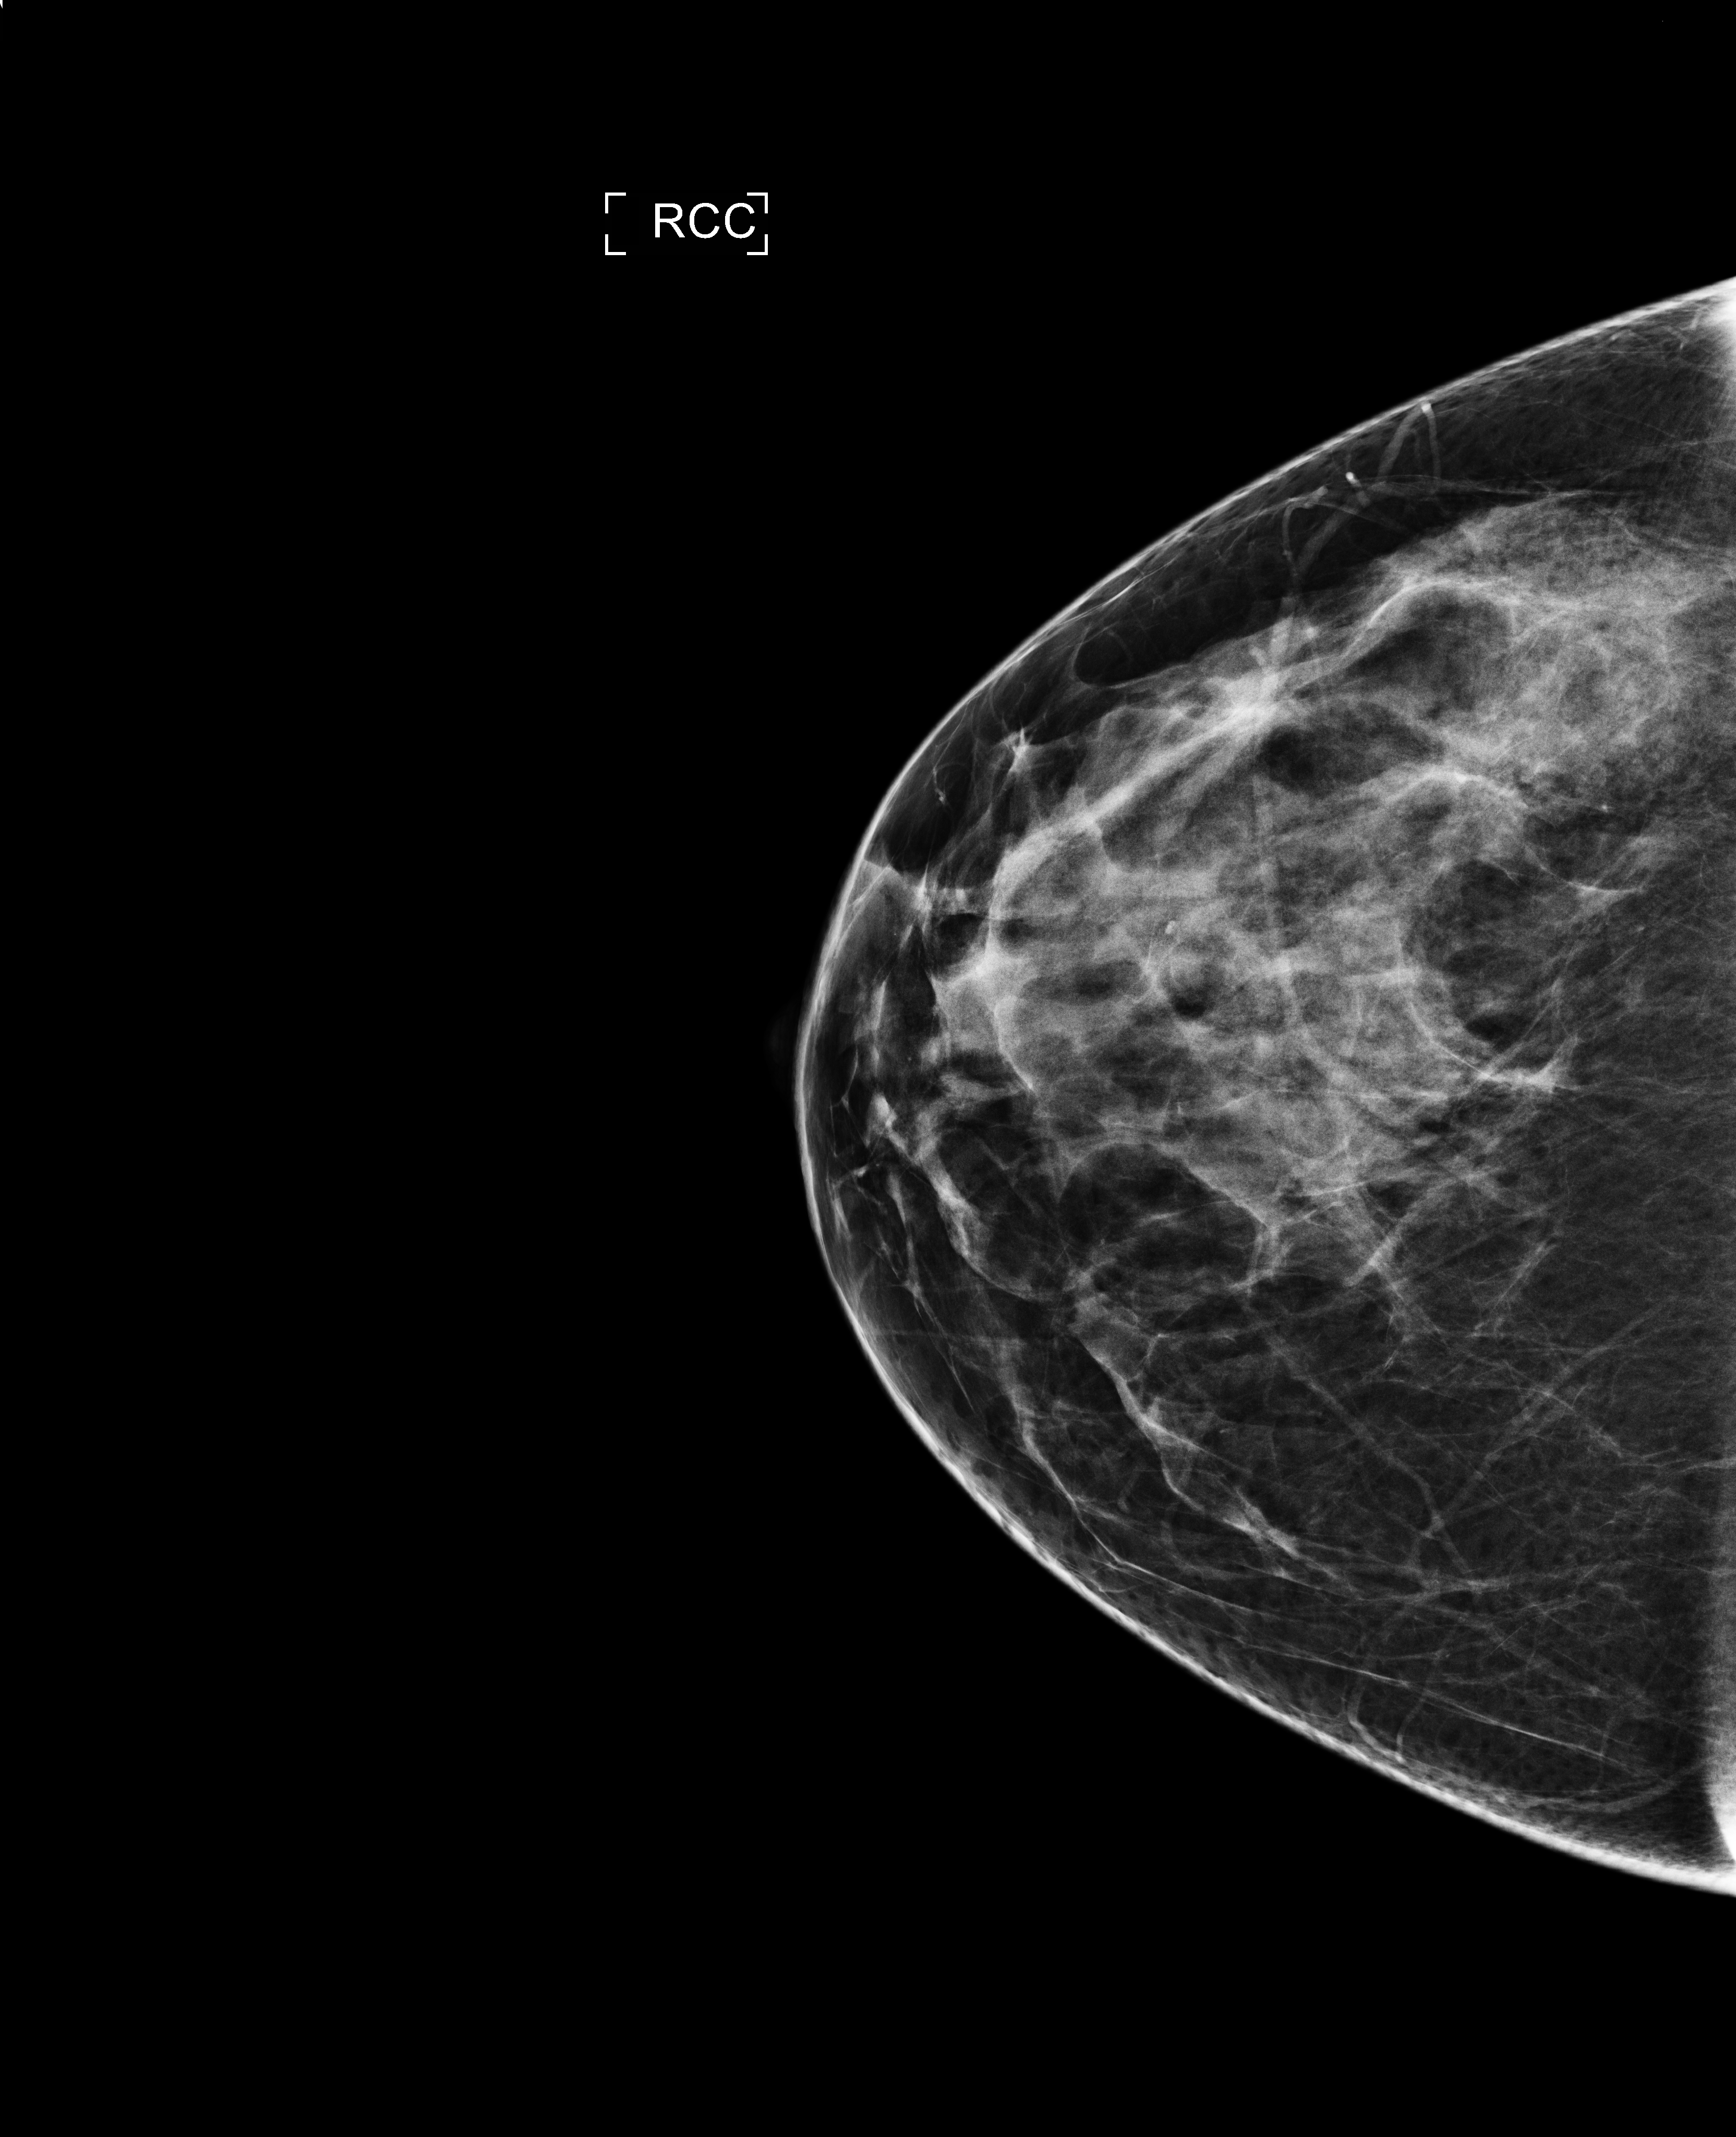
Full-field digital mammogram (FFDM), right breast, cranio-caudal projection, screening examination, compressed breast thickness 68 mm. Female patient, age 45 years.
Final BI-RADS assessment for this screening round (tomosynthesis exam, both breasts): category 1.